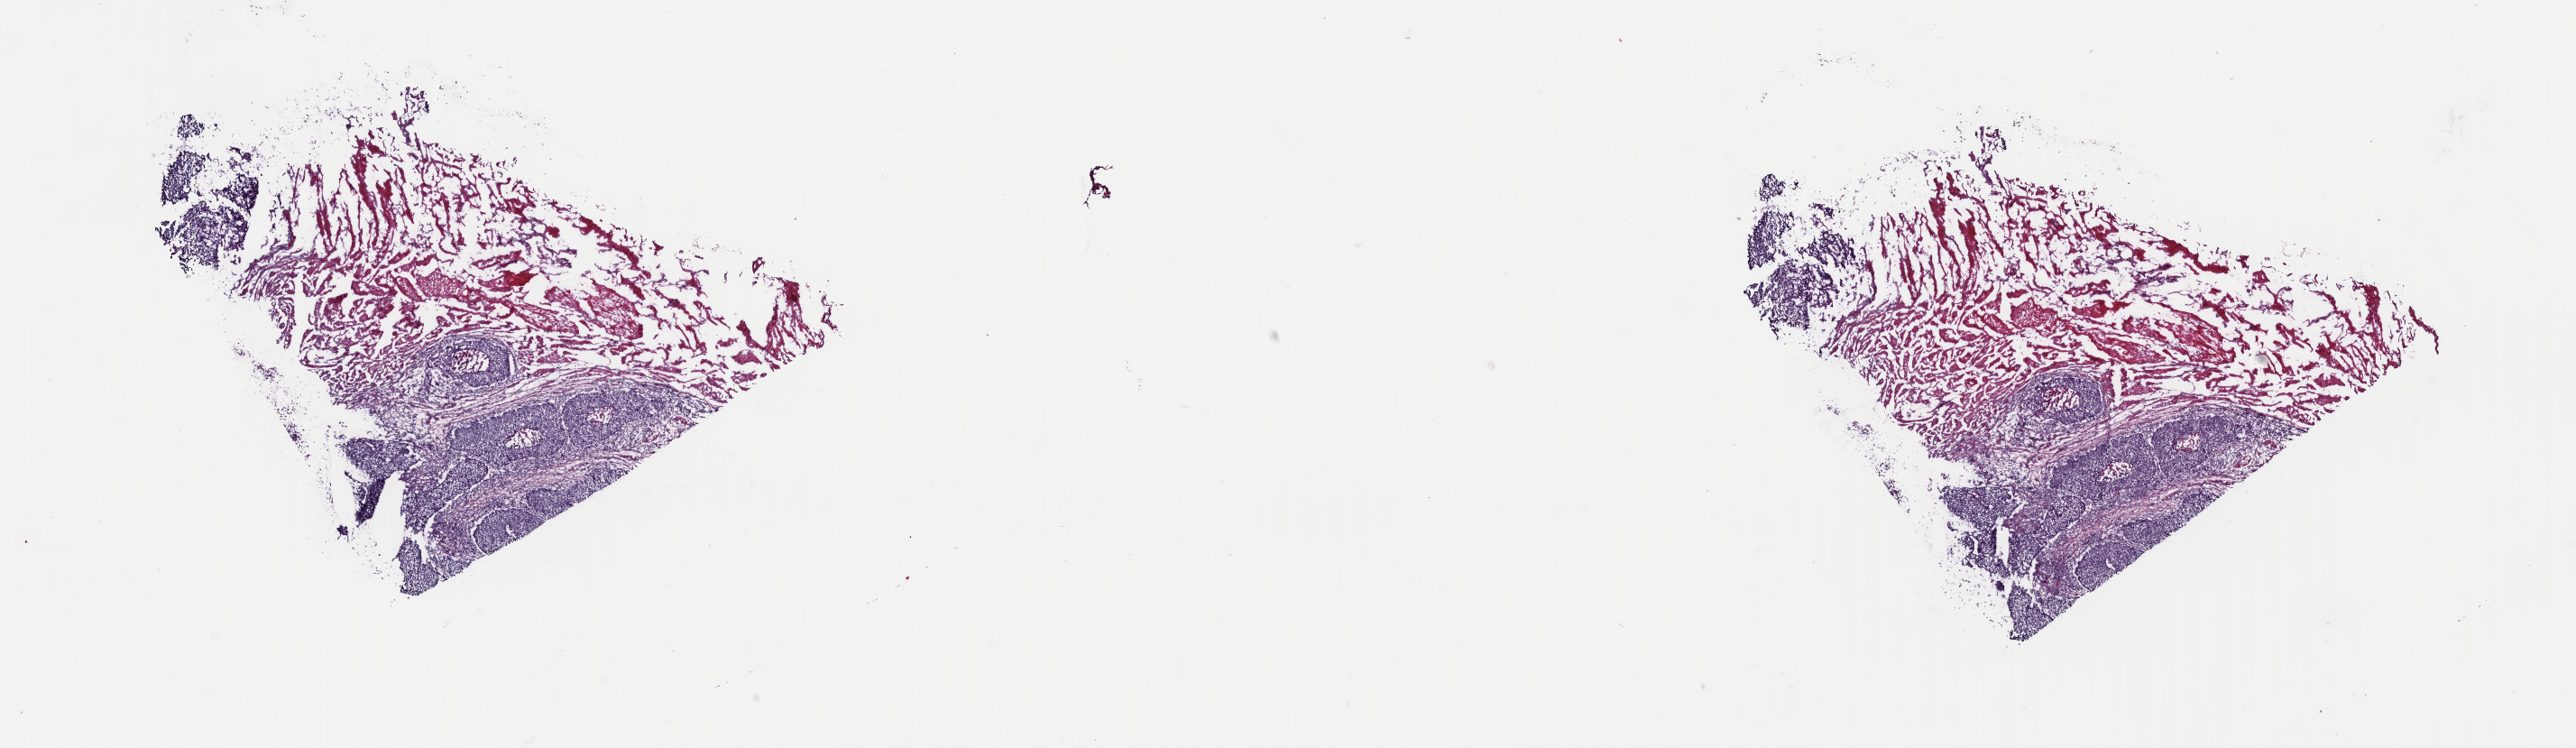
Digitized H&E-stained tissue section (whole slide) — a low-resolution overview of the entire scanned area, about 22.6 x 6.5 mm (acquisition: 40x scan), frozen section from the top of the tissue portion, esophagus, primary tumour sample. Patient: male, age at initial diagnosis 66 years. Histologic grade: G2 (moderately differentiated). Pathologist review of this section (percent, as recorded): tumour cells 70%, tumour nuclei 70%, normal cells 0%, stromal cells 27%, necrosis 3%. Inflammatory infiltration, as recorded: lymphocyte infiltration 3%, monocyte infiltration 1%, neutrophil infiltration 1%.
* AJCC pathologic stage: IIA (6th edition)
* histologic diagnosis: Squamous cell carcinoma, NOS (middle third of esophagus)